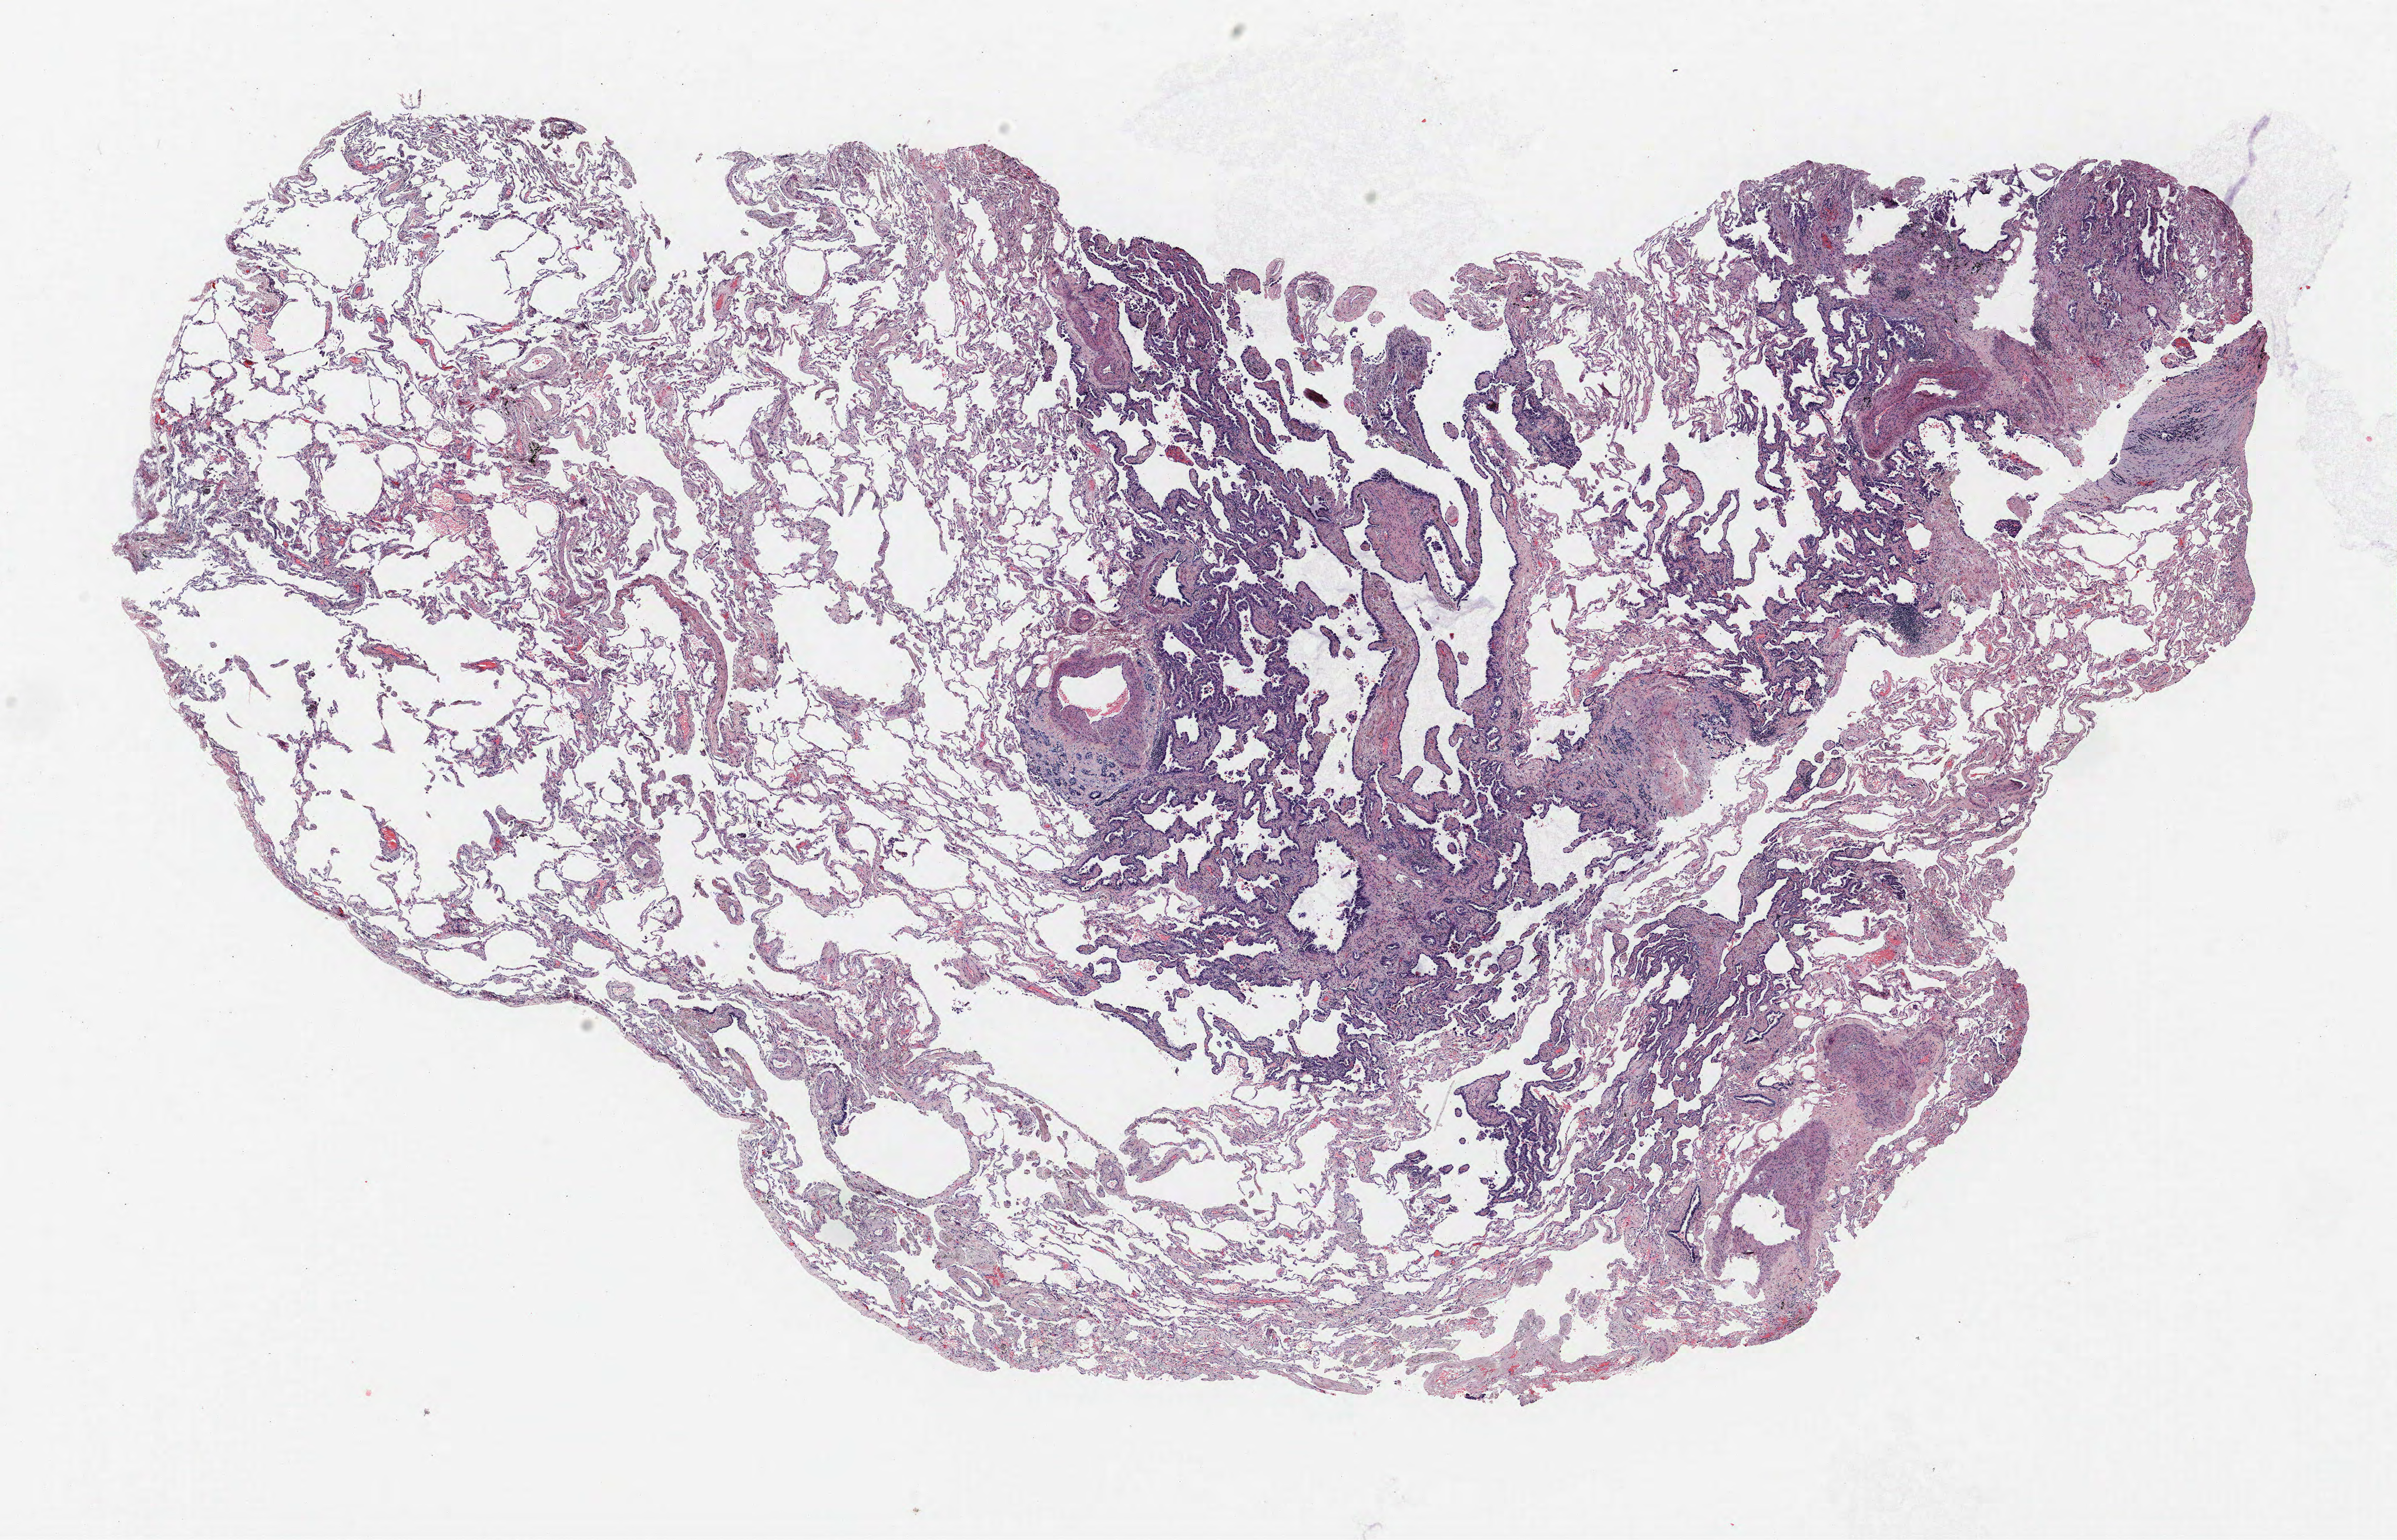
Whole-slide histology image, H&E — low-resolution overview of the scanned area, about 16.3 x 10.5 mm (slide scanned at 40x); formalin-fixed paraffin-embedded (FFPE) section; lung tissue. Female patient, aged 63 at enrolment. Grade: well differentiated (G1).
- stage (AJCC 6th edition): IA
- tumour size (pathology): 12 mm
- participant's lung-cancer diagnosis: Bronchiolo-alveolar carcinoma, non-mucinous (ICD-O-3 8252/3)
- ICD-O-3 topography: upper lobe of lung (C34.1)
- primary tumour location (clinical record): right upper lobe